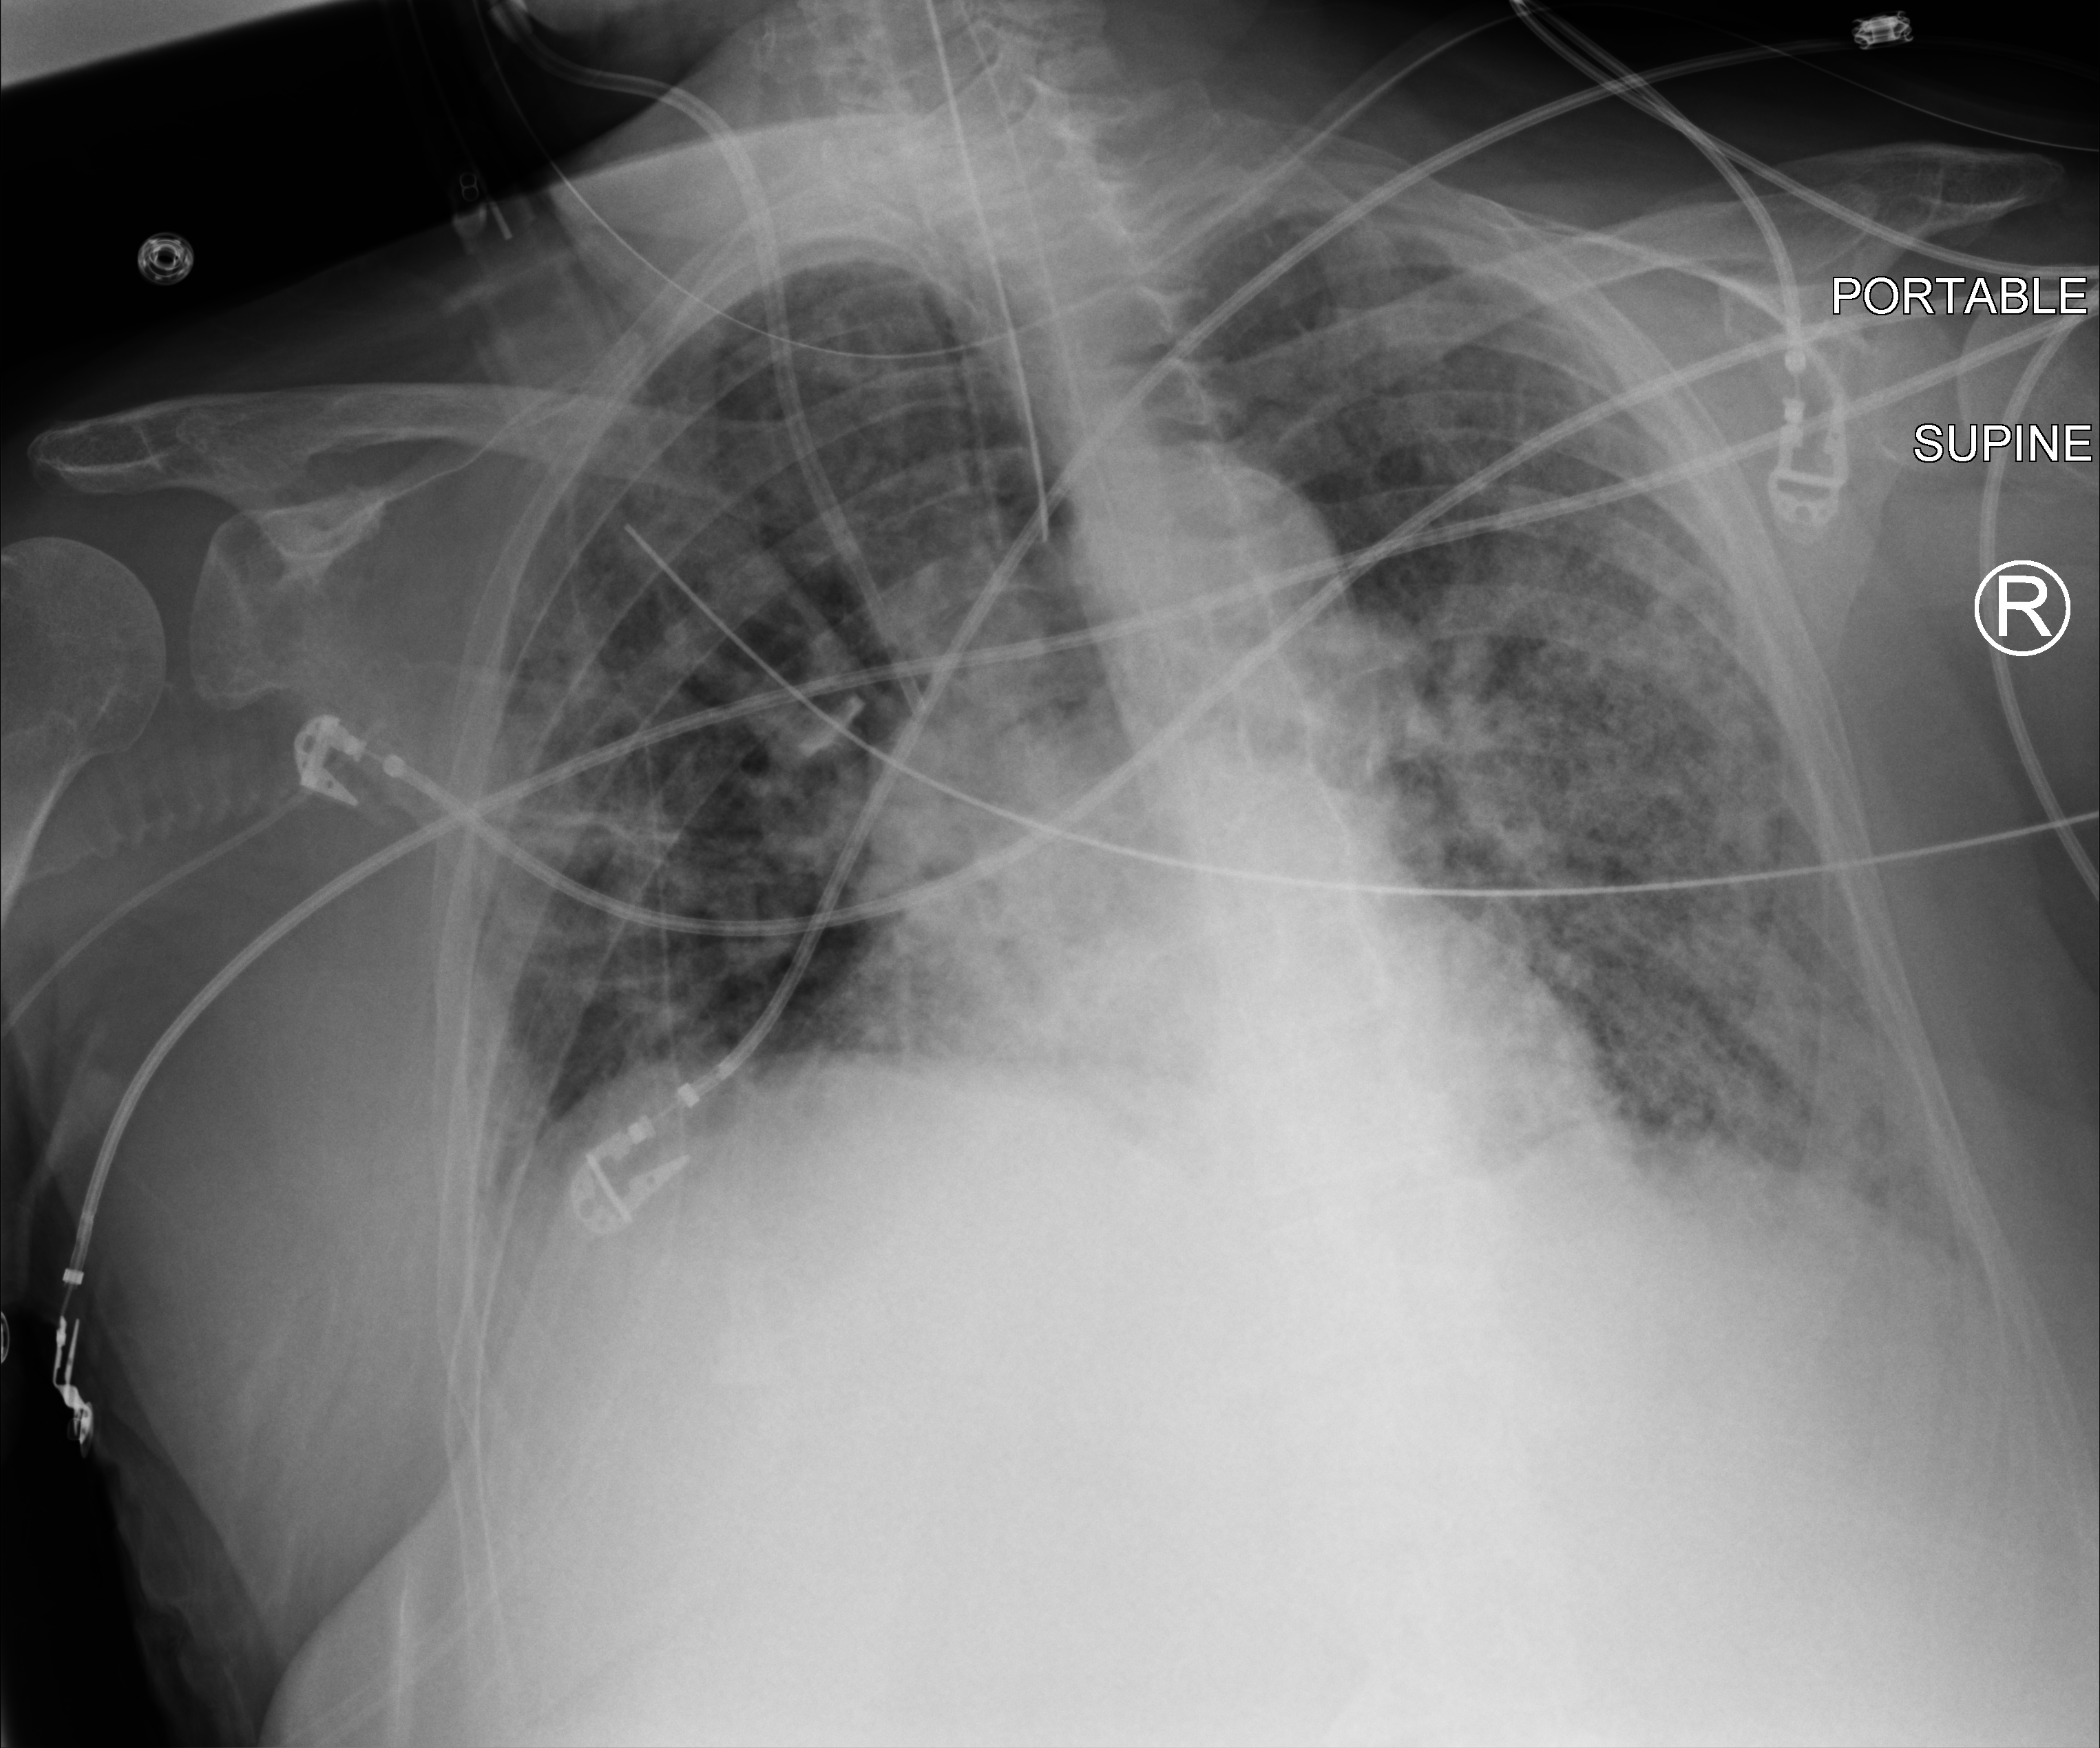
Bedside chest radiograph (computed radiography). Patient hospitalised with COVID-19; female, aged 75–90 years.
Admission-level facts for this patient (not findings on this image; timing relative to this image not recorded): hypertension (admission record): yes; mechanically ventilated during this hospital stay: yes.